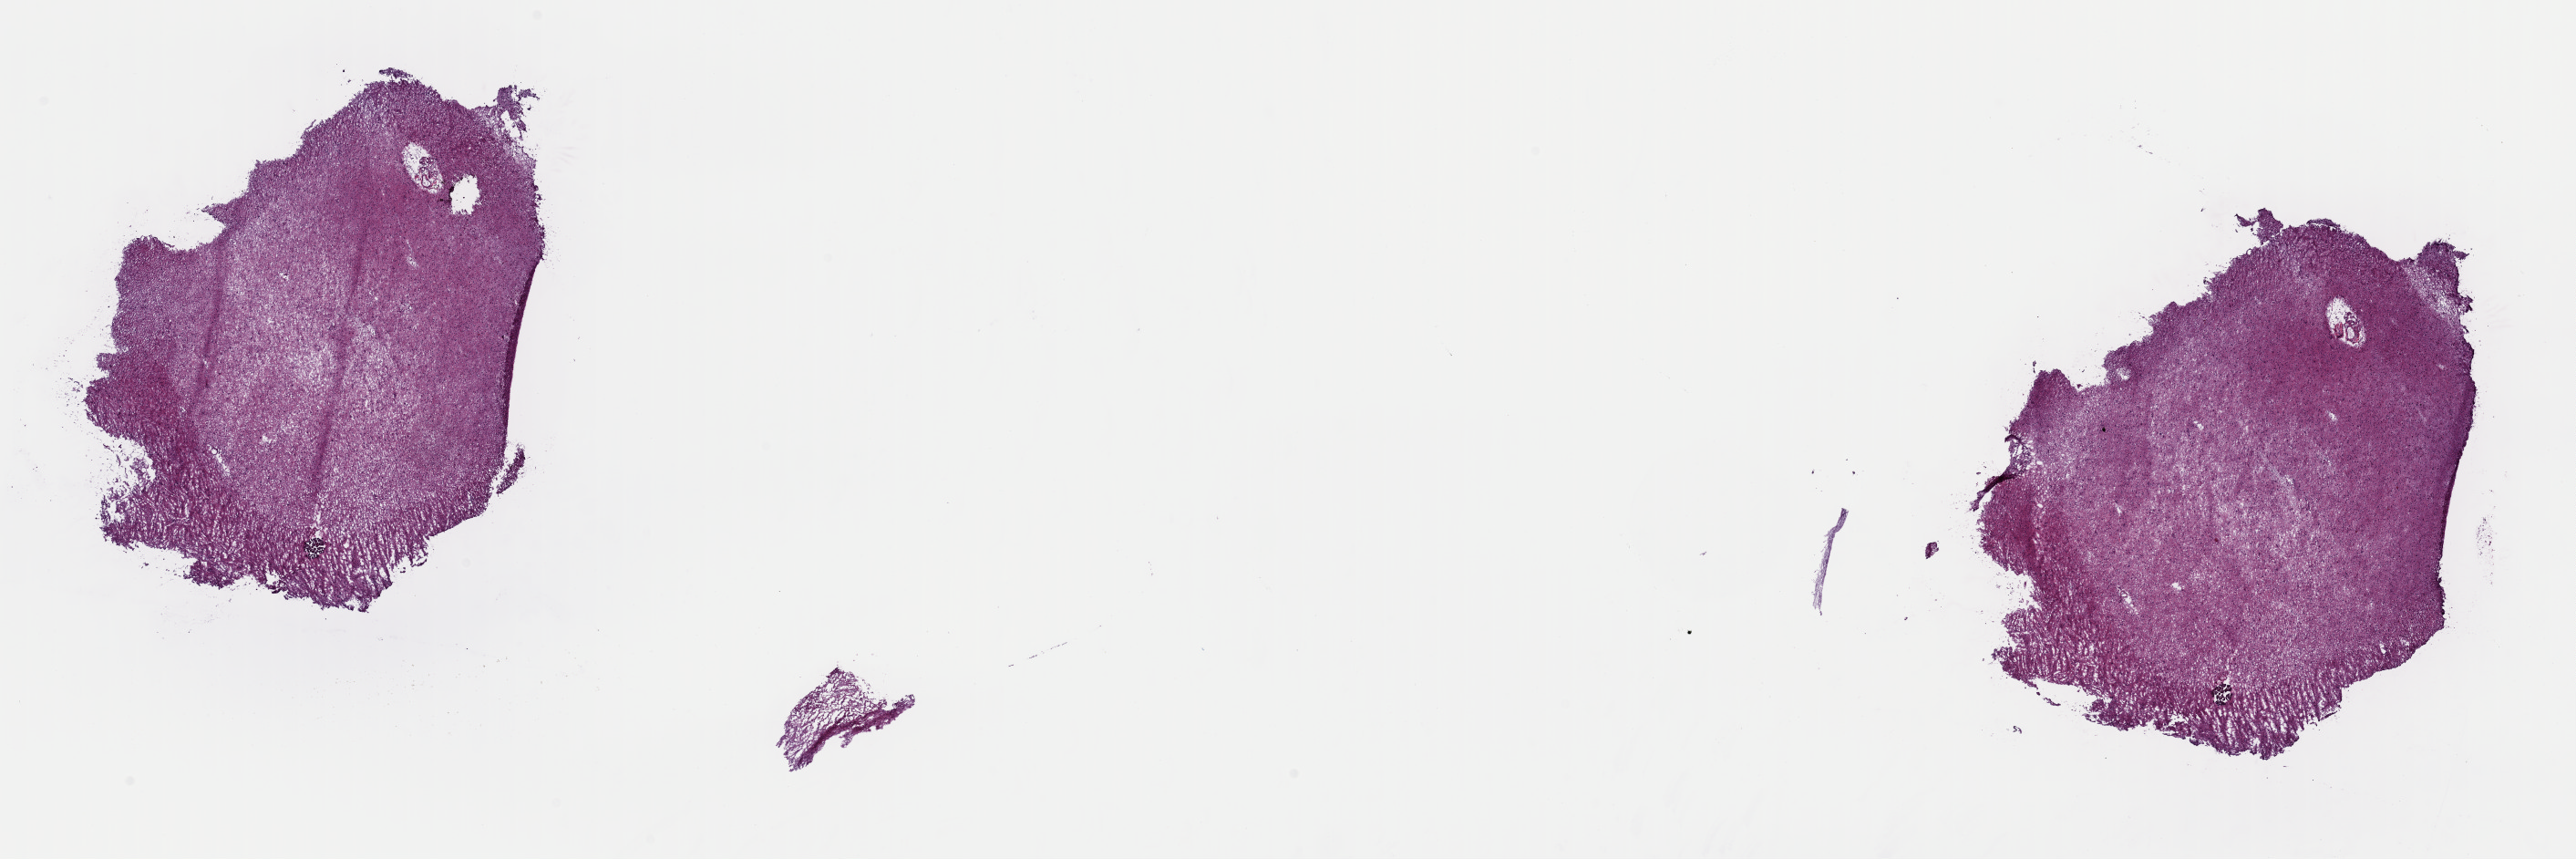
Whole-slide histology image, Hematoxylin and eosin (H&E) stained, shown as a low-resolution overview of the whole scanned area (about 22.3 x 7.4 mm, slide scanned at 40x), frozen section from the top of the tissue portion, brain, primary tumour sample. Male, age 64 years at initial diagnosis. Histologic grade: G3 (poorly differentiated). Composition of this section per pathologist review: tumour cells 60%, tumour nuclei 90%, normal cells 5%, stromal cells 35%, necrosis 0%. Inflammatory infiltration, as recorded: lymphocyte infiltration 0%, monocyte infiltration 0%, neutrophil infiltration 0%.
Pathologic diagnosis: Astrocytoma, anaplastic (cerebrum).